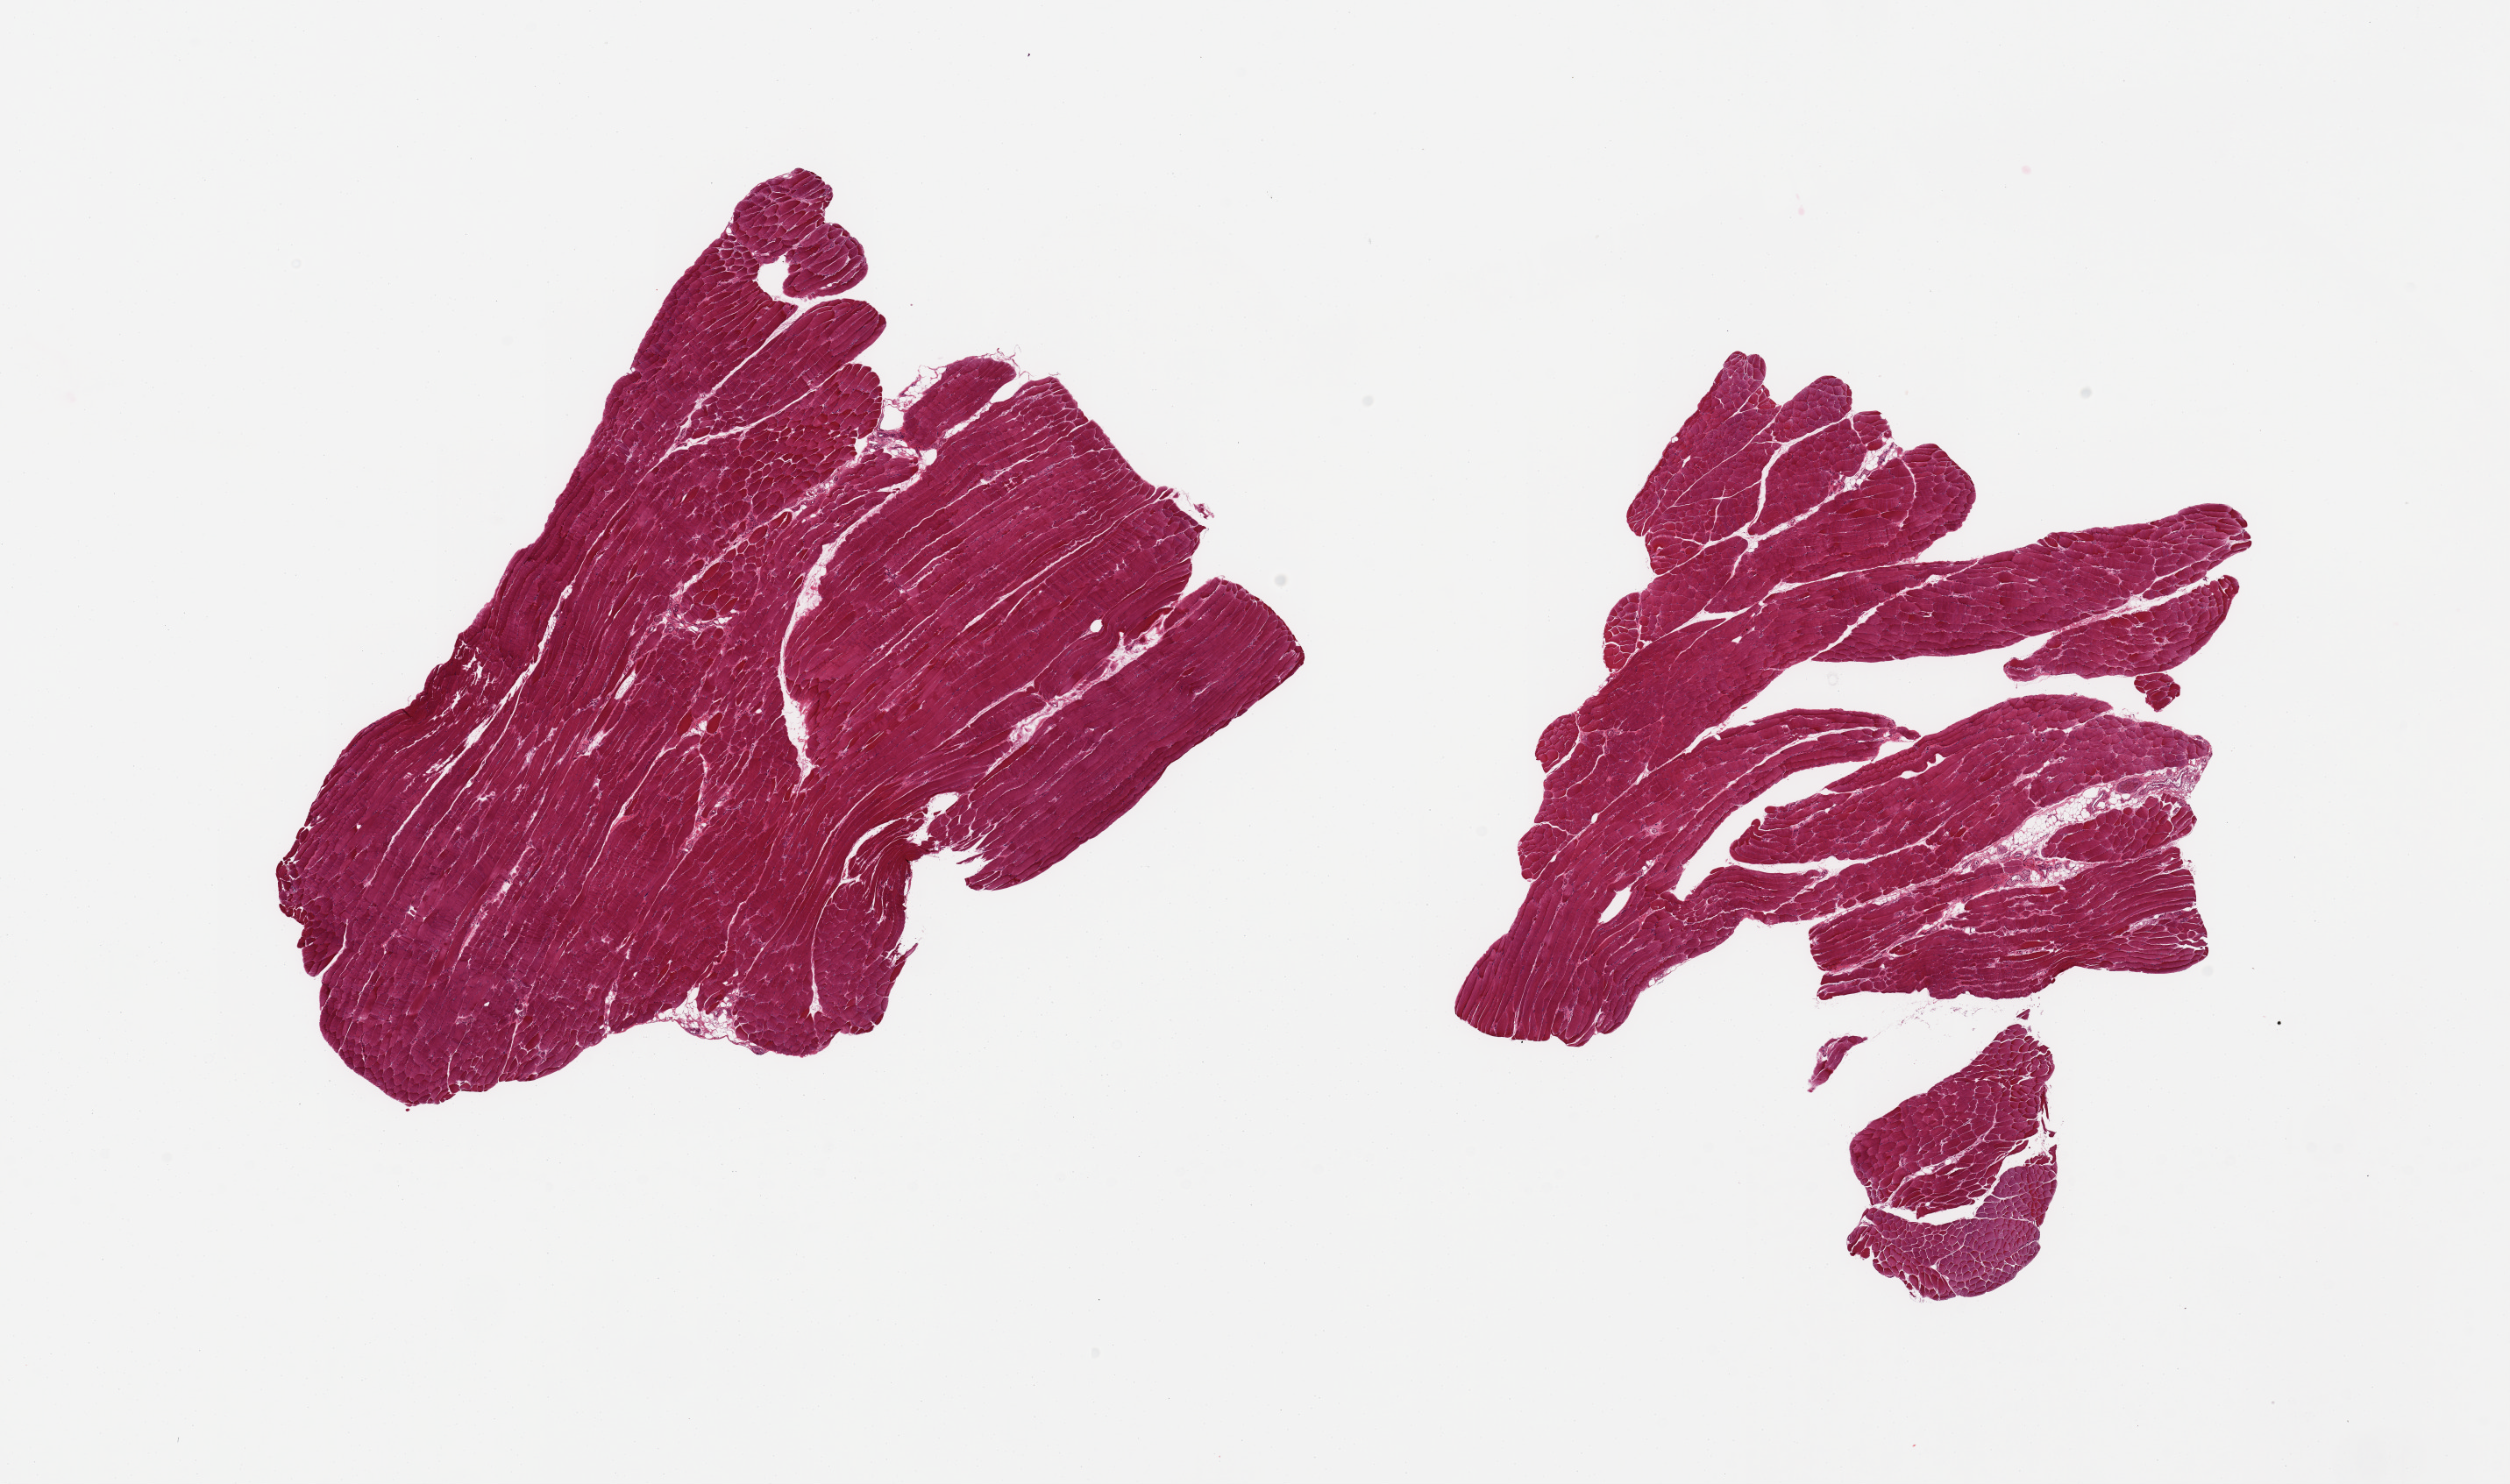
Whole-slide image, hematoxylin and eosin (H&E) stain, brightfield, low-resolution overview of the scanned area, about 22.6 x 13.4 mm (acquisition: 20x scan); PAXgene-fixed, paraffin-embedded tissue; target tissue: skeletal muscle; donor tissue sample. Donor sex: female.
Review note (as recorded): 2 pieces; minimal fat.